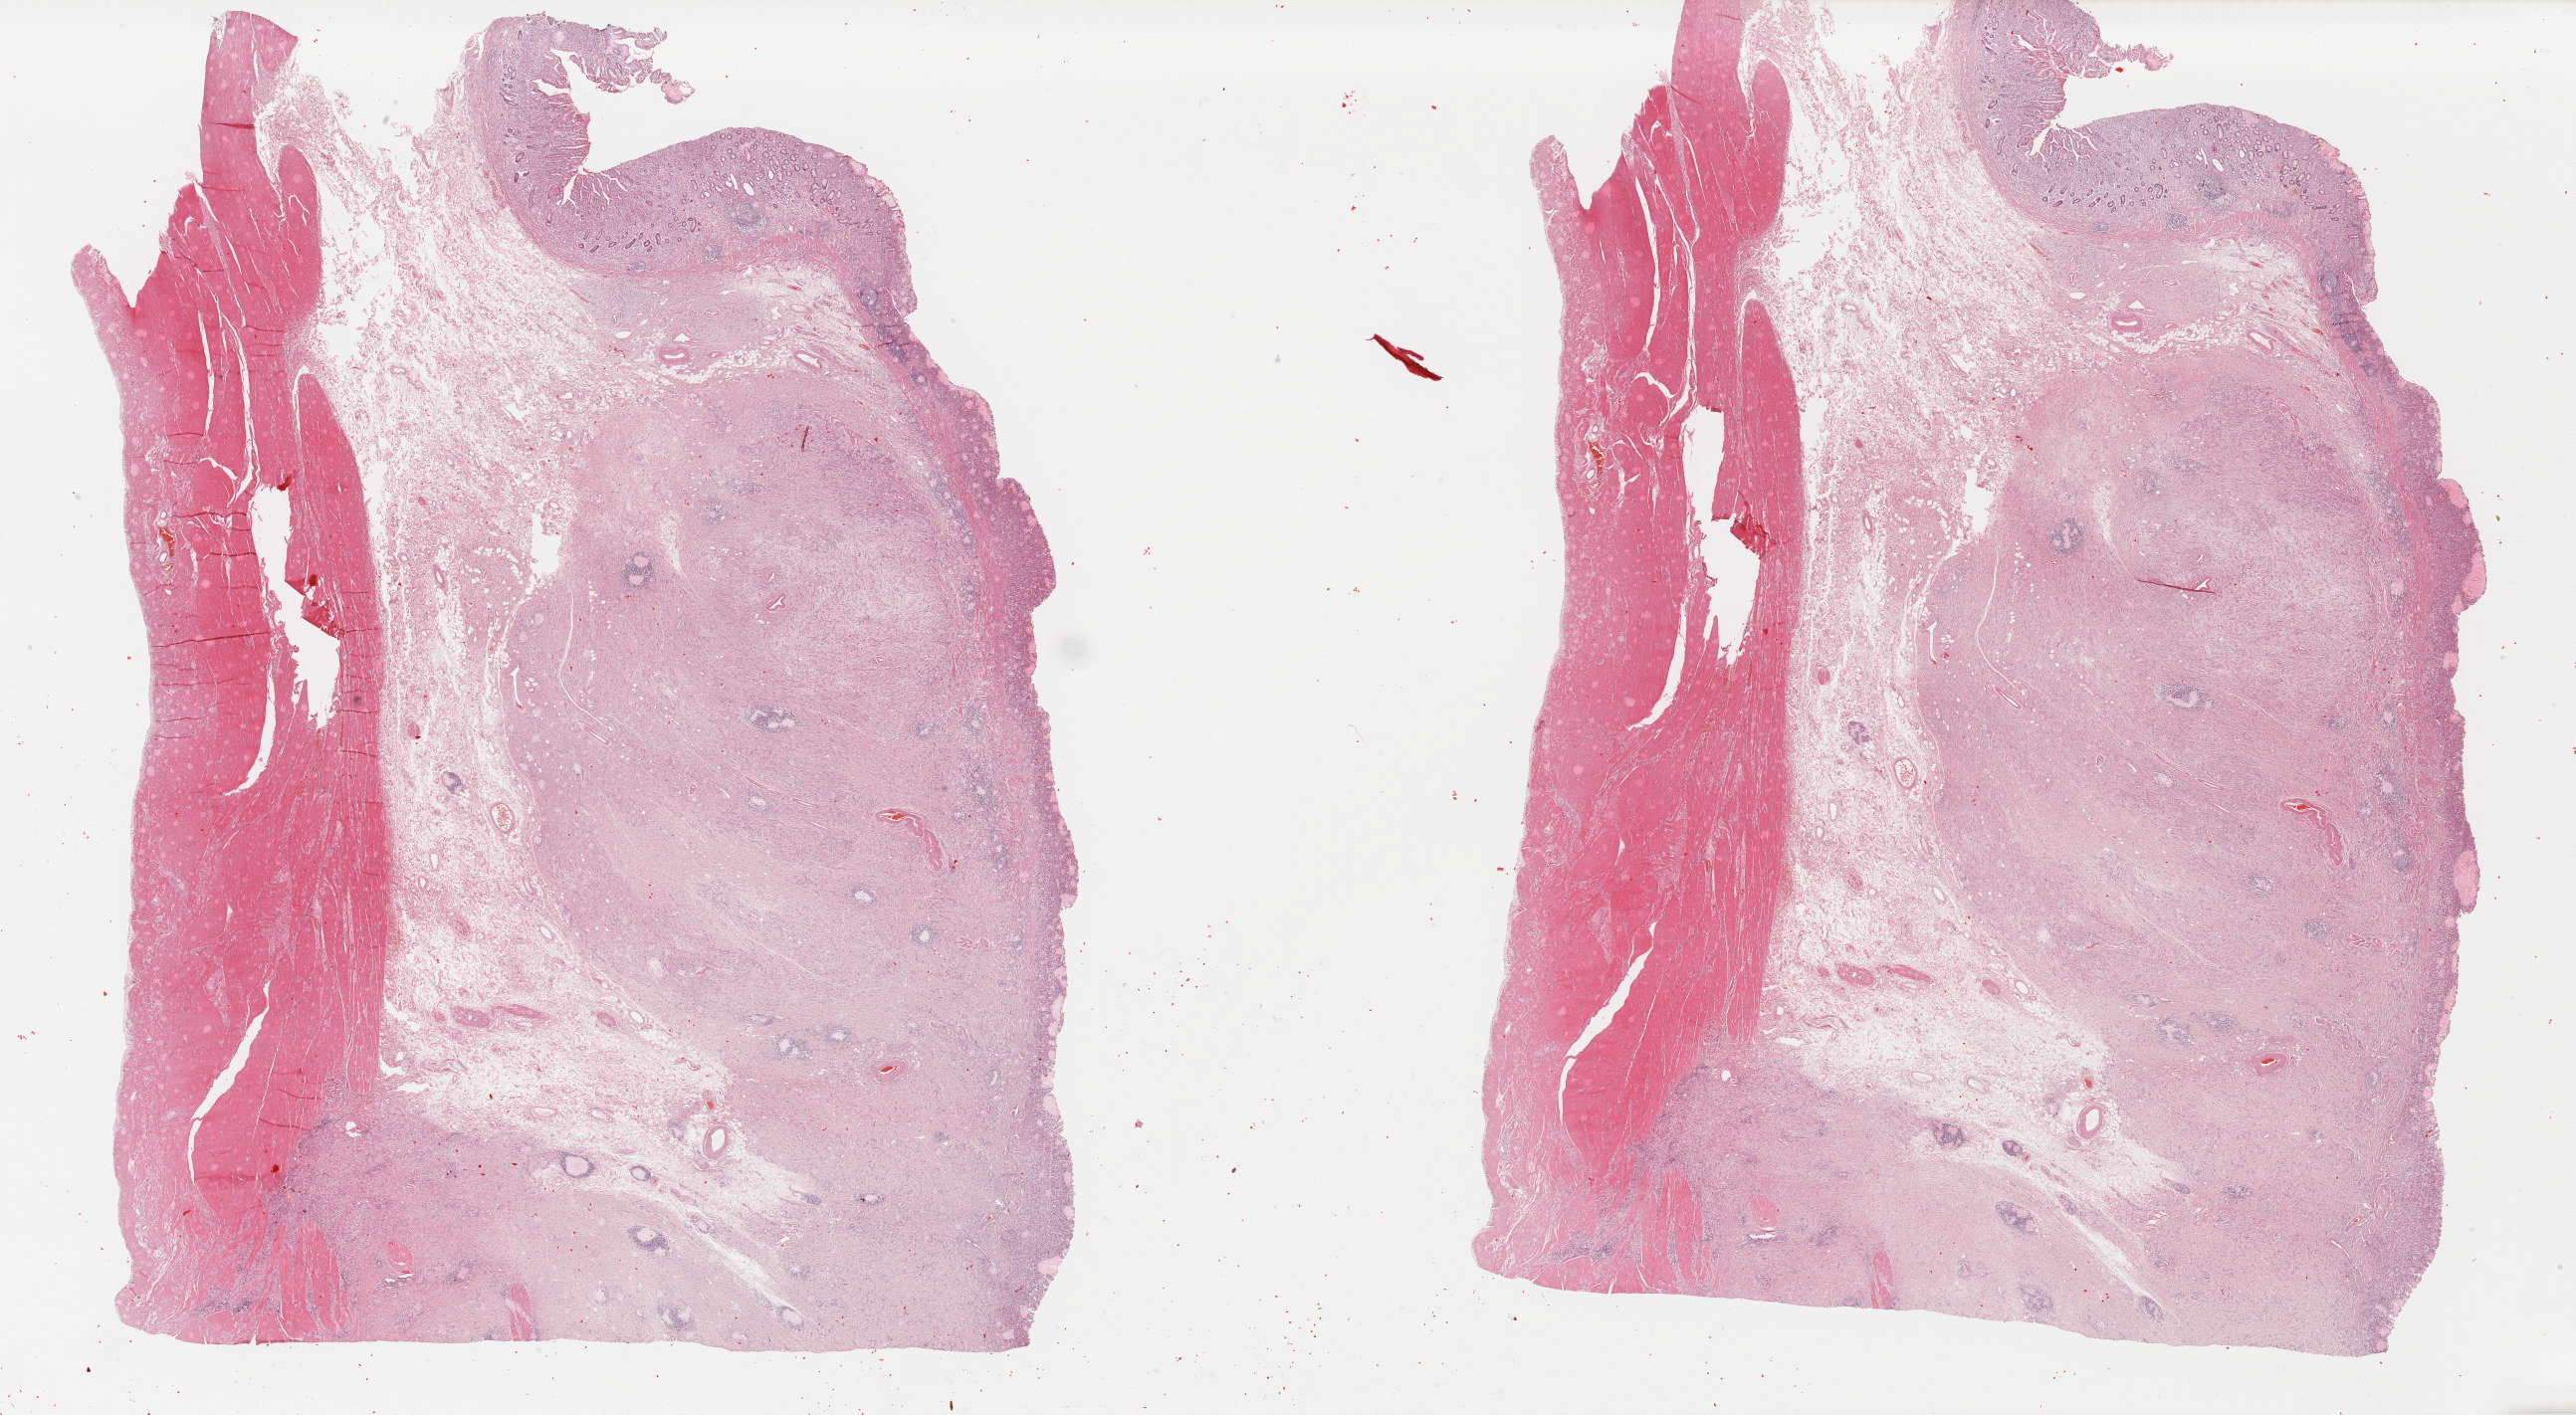
H&E whole-slide image — whole scanned area (about 40.7 x 22.4 mm) shown as a low-resolution overview, formalin-fixed paraffin-embedded (FFPE) diagnostic section, primary tumour sample from the stomach. Patient: male, age at initial diagnosis 53 years. Histologic grade: G3 (poorly differentiated).
AJCC pathologic stage: II (6th edition). Pathologic diagnosis: Carcinoma, diffuse type. Lymph nodes positive (case pathology): 6 of 16 examined.